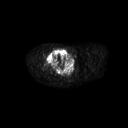
FDG PET of an extremity soft-tissue mass (from a PET/CT study), one axial slice. Position 265 of 311 along the scan axis. 3.27 mm slice thickness. 128 × 128 image matrix, field of view 700 × 700 mm. Patient: male, 50 years. From the clinical record (not read from this slice): histological type: undifferentiated - pleiomorphic; grade: high; site of the primary tumour: right thigh.
Annotated regions visible in this slice (expert contour drawn on MRI and transferred to this co-registered scan by the dataset authors):
- gross tumour volume including surrounding oedema: bounding box <45,48,67,68> (left, top, right, bottom; pixels)
- gross tumour volume (mass): <46,48,67,68>